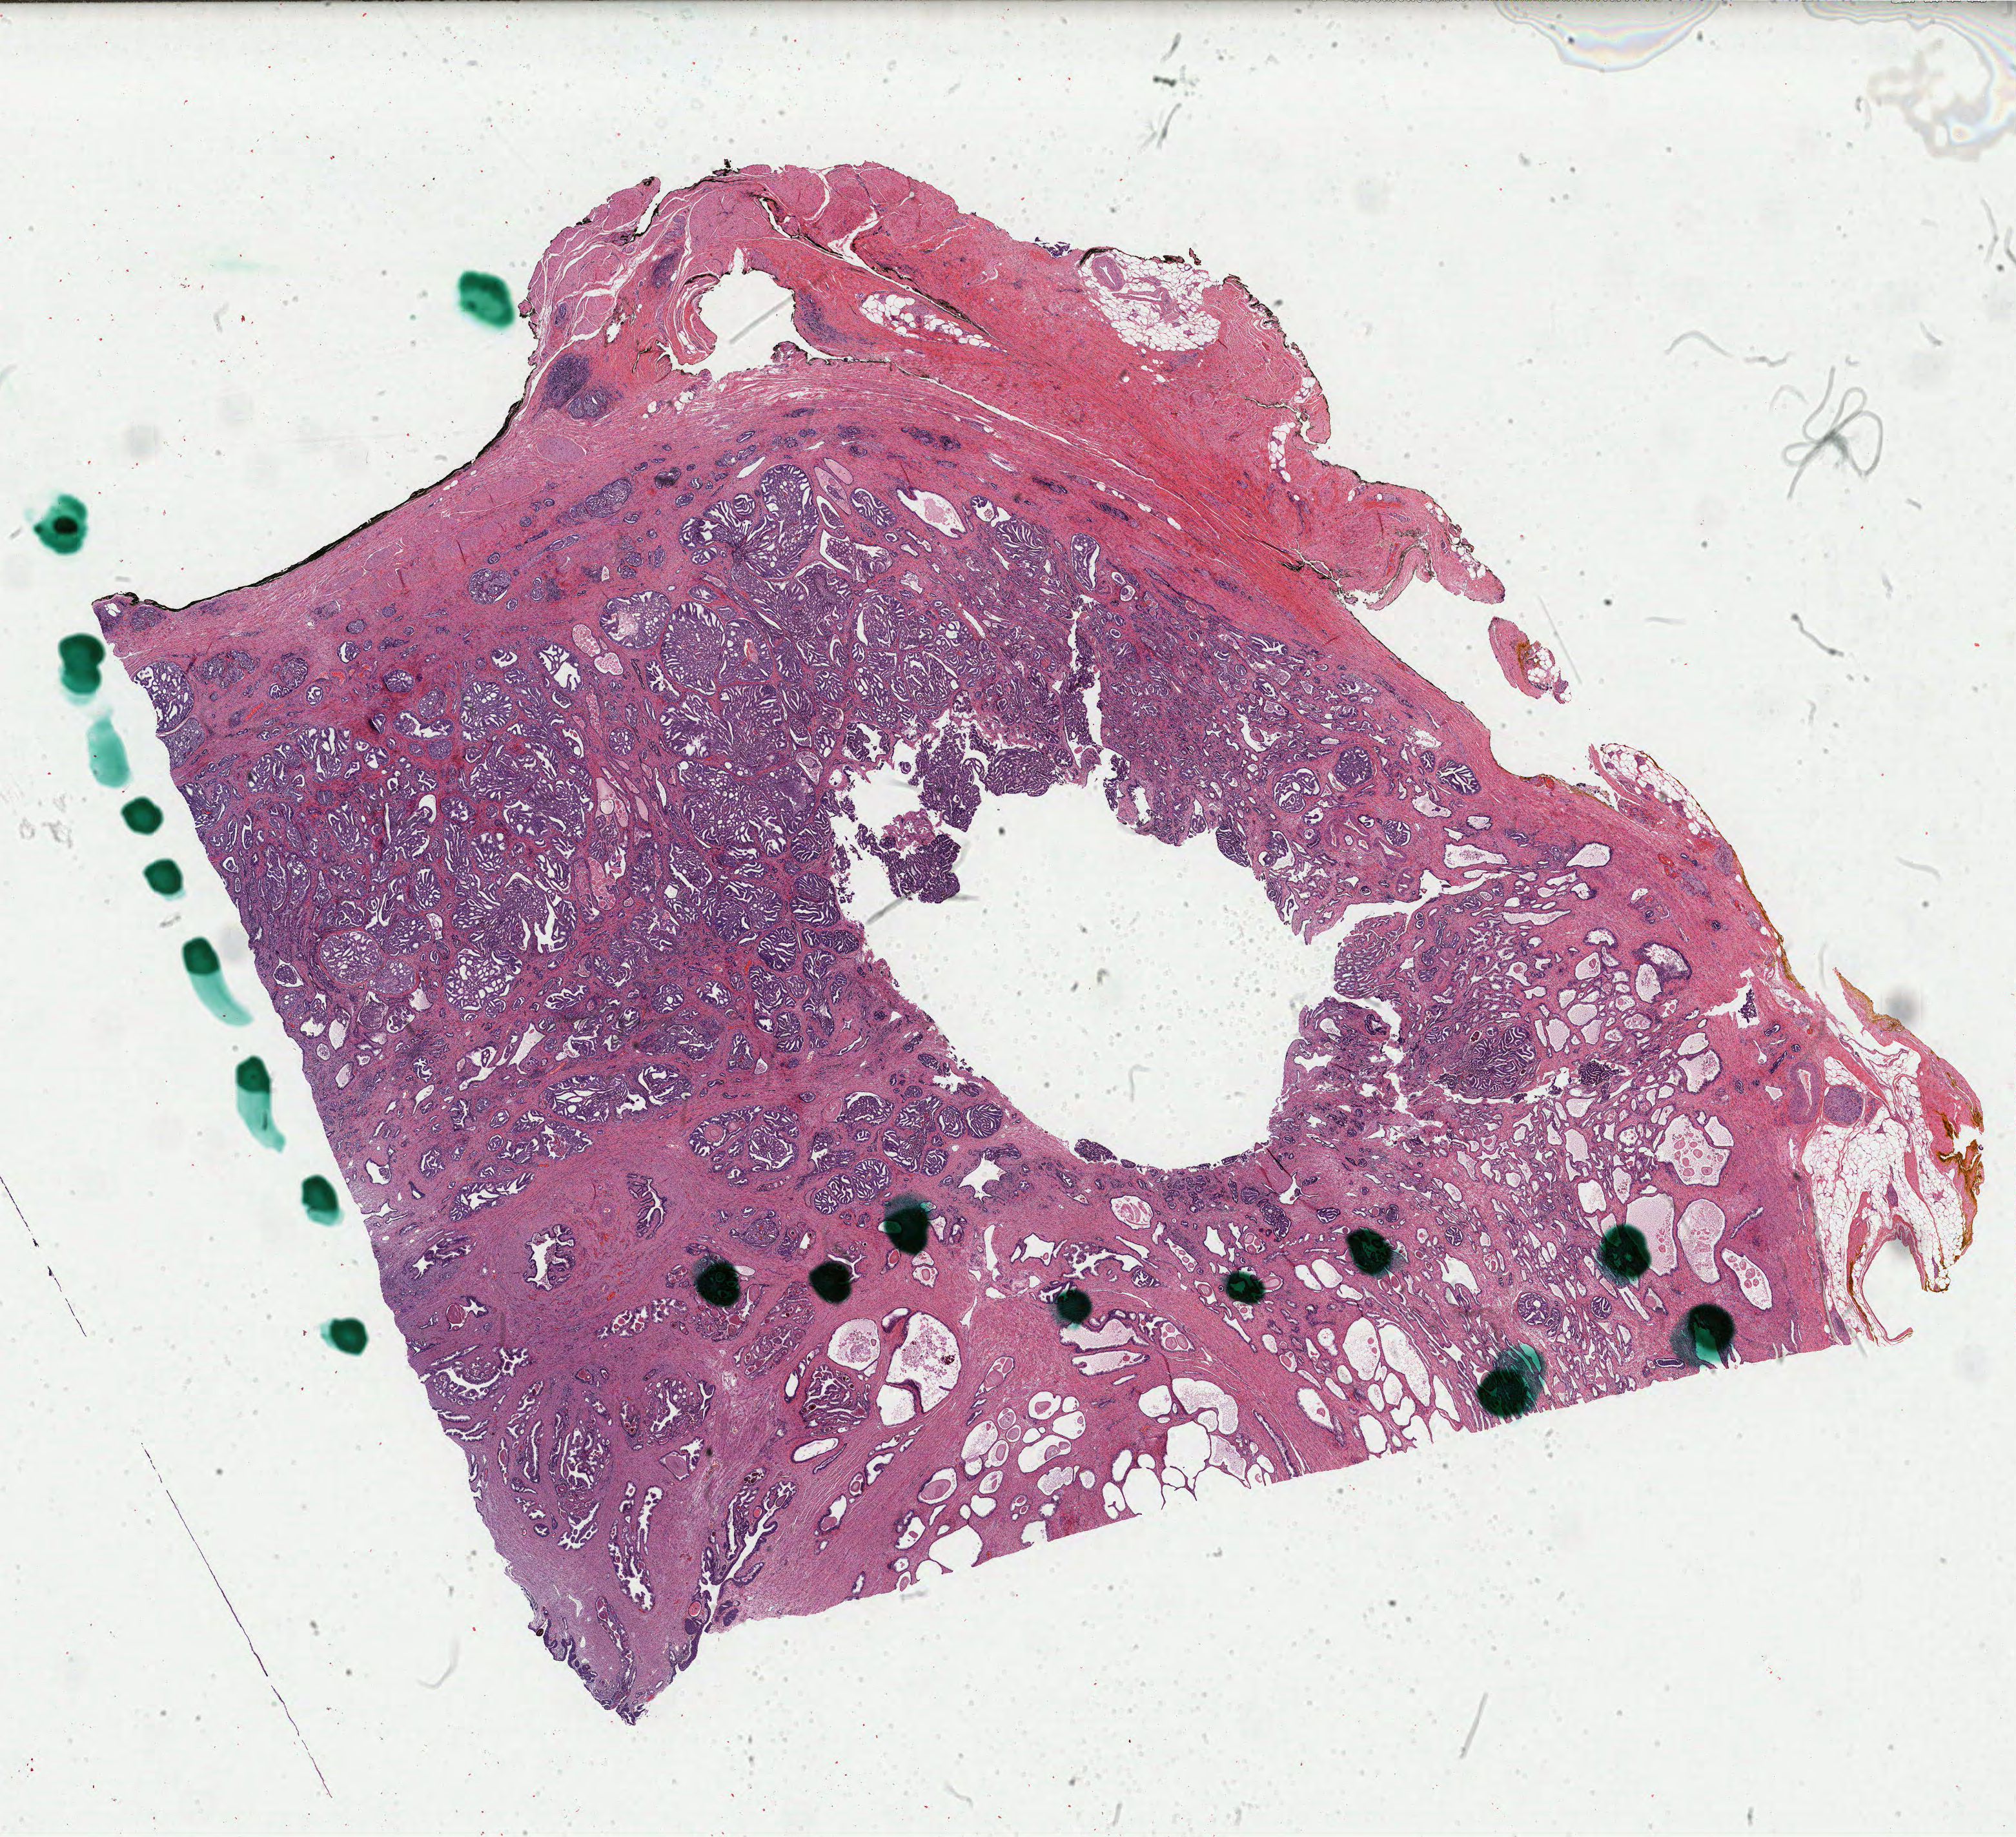
H&E-stained whole-slide image — shown as a low-resolution overview of the whole scanned area (about 24.8 x 22.6 mm, from a 40x scan); formalin-fixed paraffin-embedded (FFPE) diagnostic section; prostate, primary tumour sample. Male patient; age at initial diagnosis 63 years. Gleason score: 9 (4+5).
Laterality: bilateral. Lymph nodes positive (case pathology): 3 of 11 examined. Pathologic diagnosis: Adenocarcinoma, NOS (prostate gland).